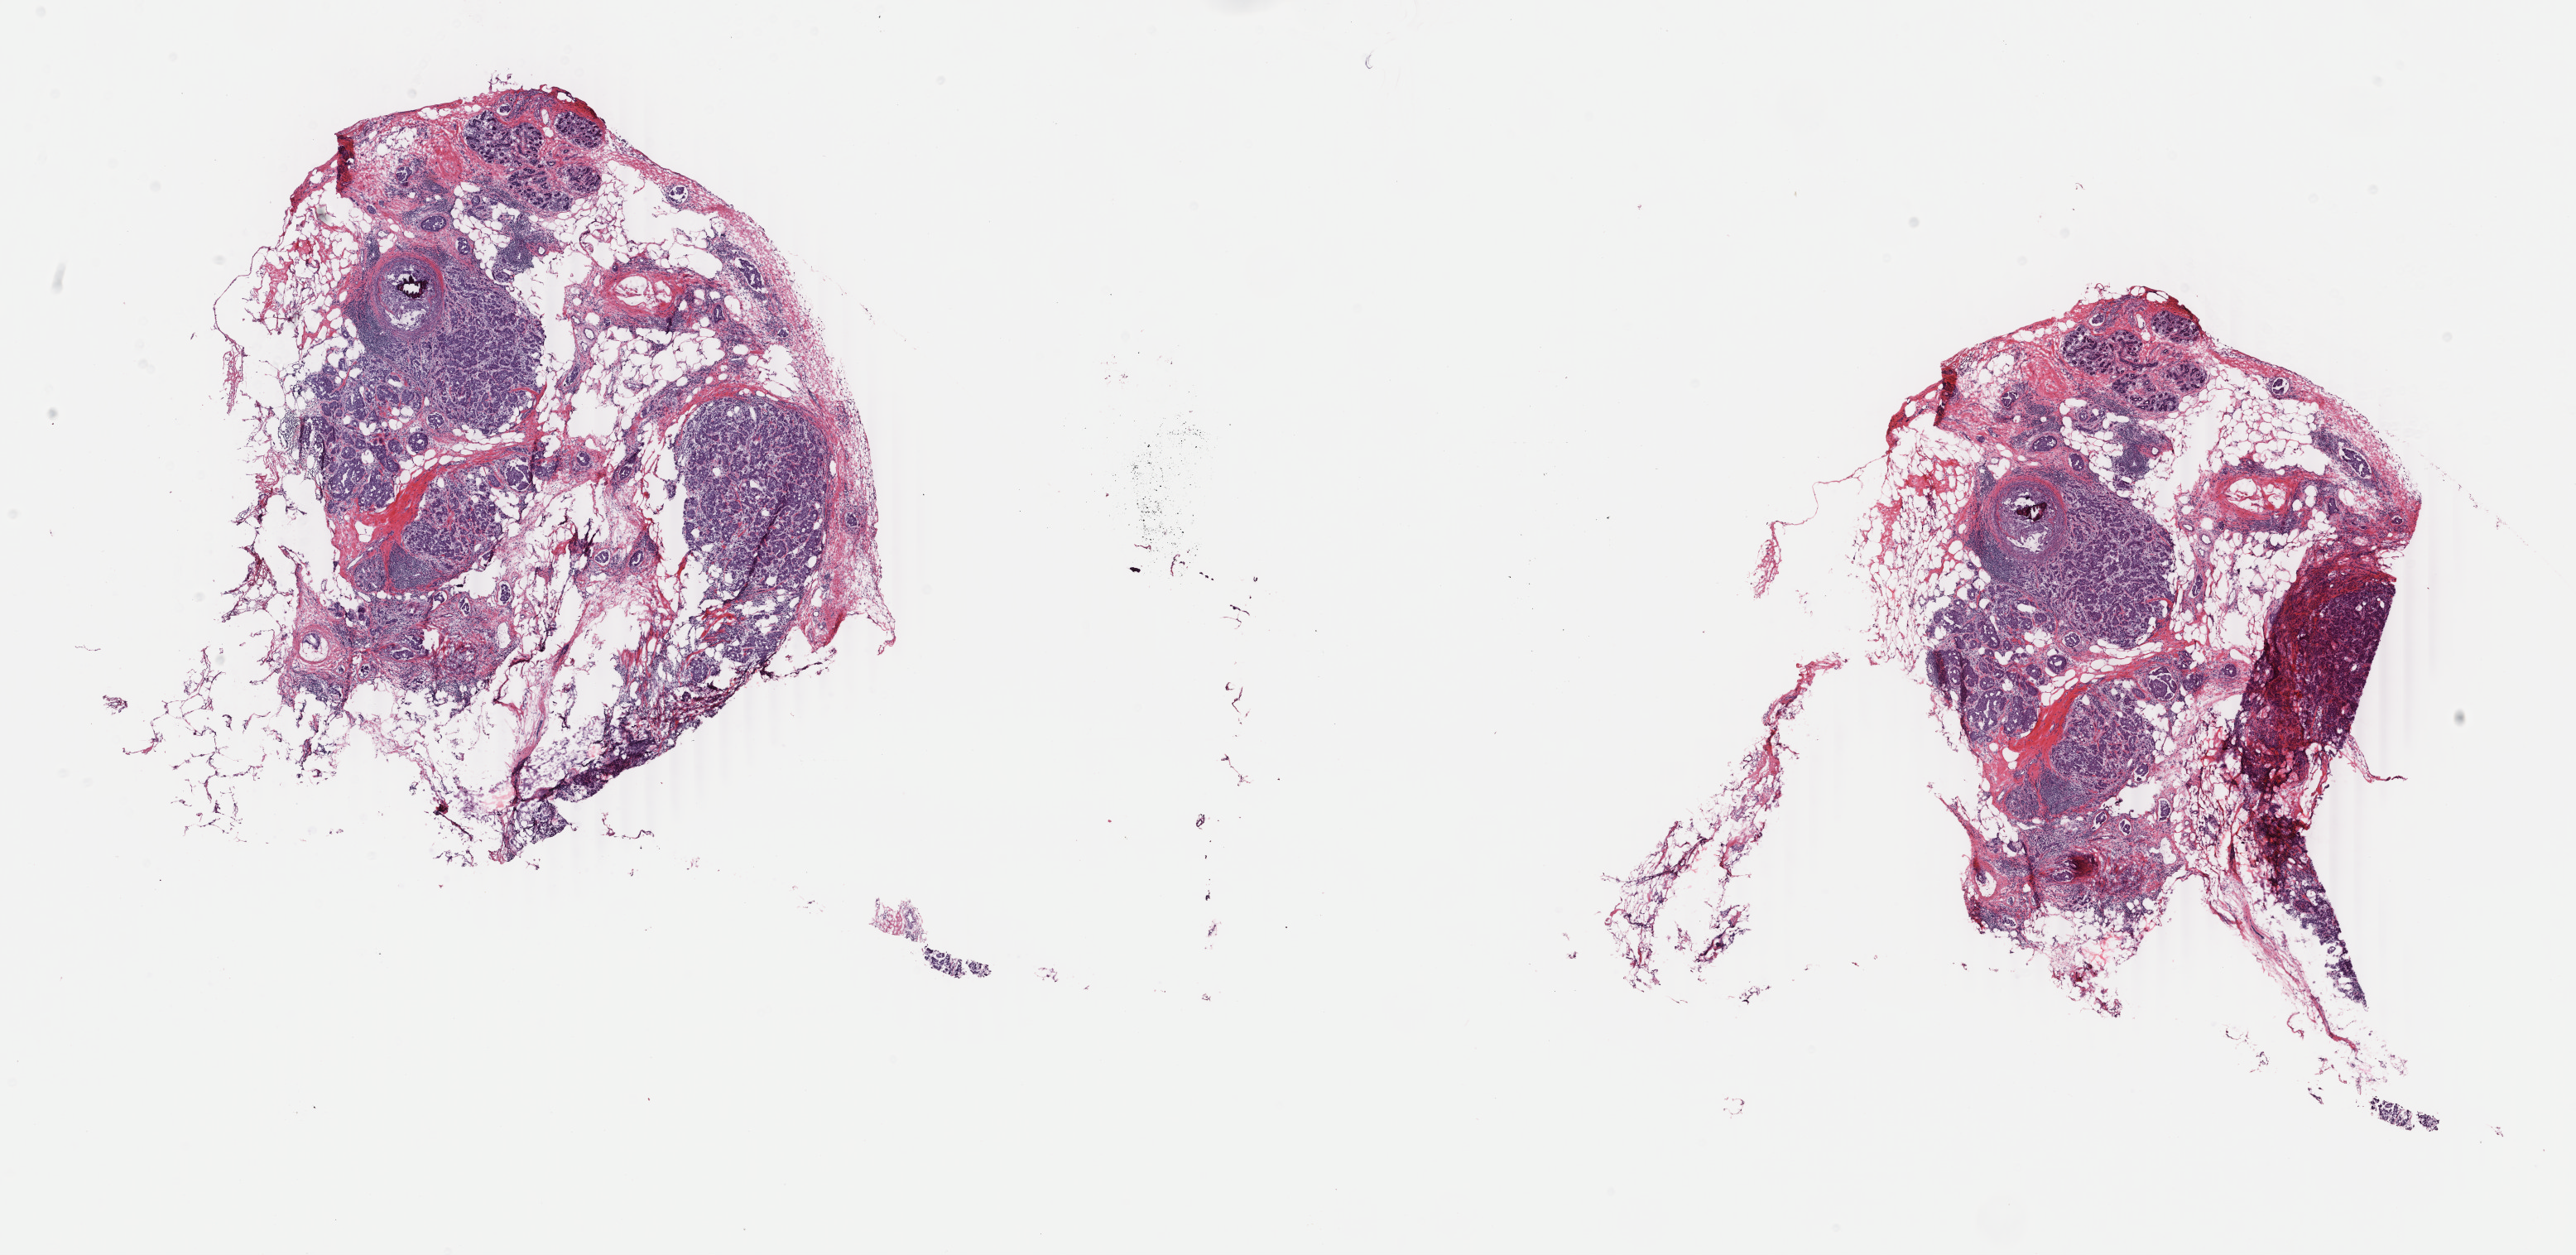
Whole-slide histology image, H&E-stained — shown as a low-resolution overview of the whole scanned area (about 24.7 x 12.1 mm, acquisition: 40x scan). Frozen section. Primary tumour sample from the breast. Patient: female, age at initial diagnosis 27 years. Slide review estimates, as recorded: tumour cells 50%, tumour nuclei 70%, normal cells 10%, stromal cells 40%, necrosis 0%. Inflammatory infiltration, as recorded: lymphocyte infiltration 0%, monocyte infiltration 0%, neutrophil infiltration 0%.
AJCC pathologic stage: IIIA (6th edition). Laterality: right. TNM: T3 N1 M0. Lymph nodes positive (case pathology): 2 of 15 examined. Diagnosis: Infiltrating duct carcinoma, NOS.